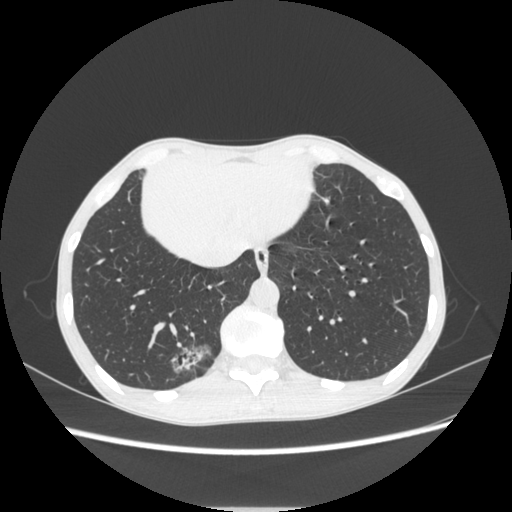
Chest CT, one axial slice; position 69 of 272 along the scan axis; 120 kVp; lung window (W 1500 / L -600 HU); 1.25 mm slice thickness; 512 × 512 image matrix, field of view 350 × 350 mm. Female patient, age 51 years. Case-level facts recorded for this patient, not image findings: clinical TNM (as recorded): T1c N0 M0; histopathological grade: G2-3.
Structures marked on this image (bounding box drawn by a radiologist):
- lung tumour (recorded histology: adenocarcinoma): bounding box (x1, y1, x2, y2) in pixels: (160, 333, 218, 386)